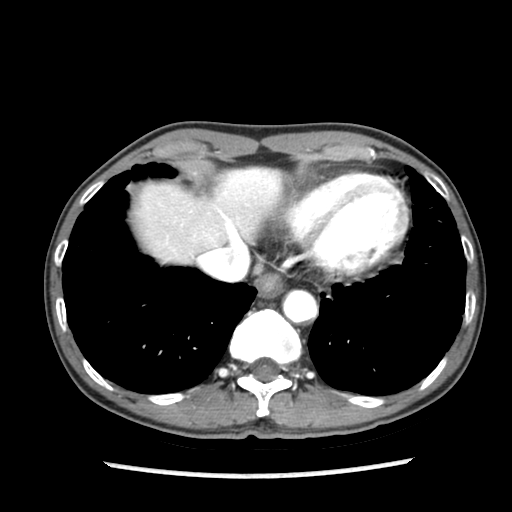
Contrast-enhanced abdominal CT (liver protocol), one axial slice. Slice 73 of 87 in the series (ordered by position). Reconstruction kernel STANDARD. 140 kVp. Soft-tissue window (W 400 / L 40 HU). 2.5 mm slice thickness. 512 × 512 image matrix, field of view 300 × 300 mm. From the clinical record (not read from this slice): diagnosis: hepatocellular carcinoma (patient treated with transarterial chemoembolisation; whether this scan precedes or follows treatment is not stated here); TNM stage (as recorded): Stage-IIIB; Child-Pugh class: A; tumour differentiation: well differentiated; tumour nodularity: uninodular.
Annotated regions visible in this slice (semi-automatic segmentation, software-assisted and operator-edited):
- liver parenchyma outside the tumour (the mass and vessels are separate outlines, so this box may not span the whole liver): bounding box [x1, y1, x2, y2] px = [134, 168, 282, 262]
- liver vessels: [222, 177, 256, 240]